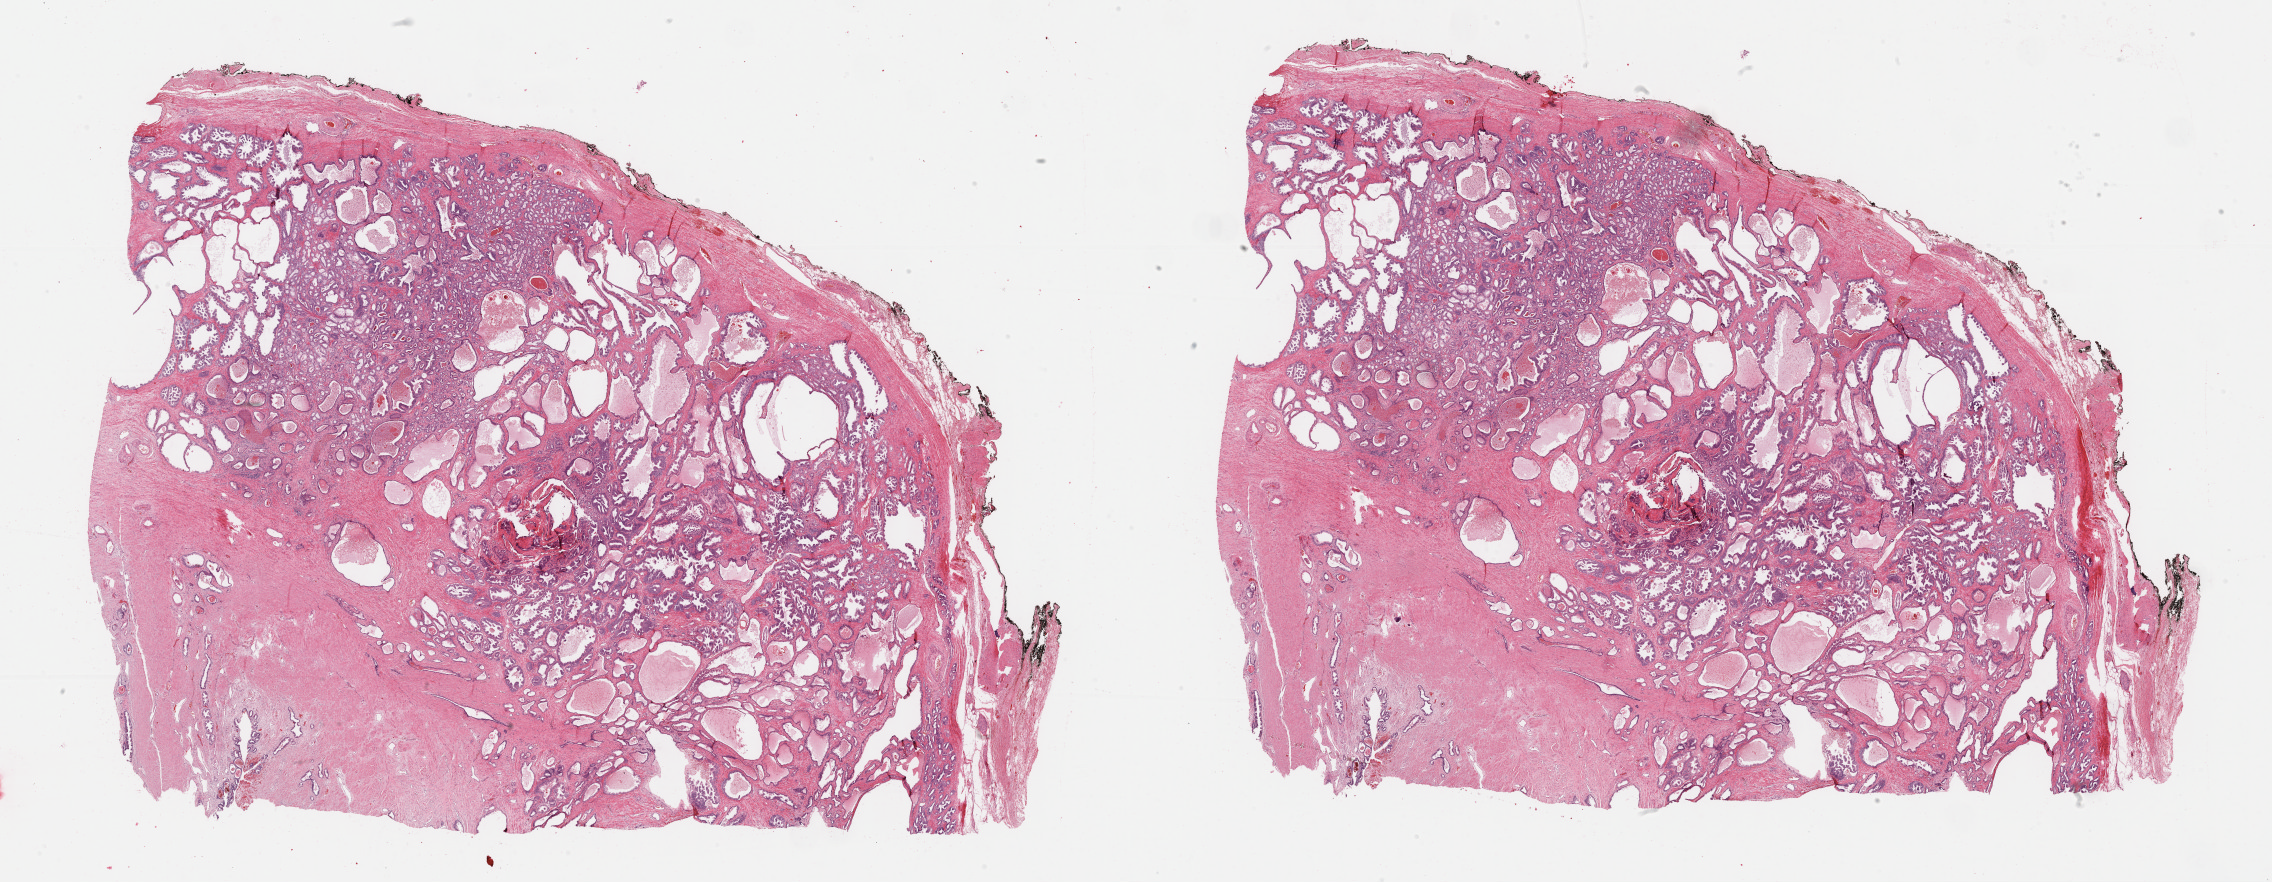
H&E-stained whole-slide image, whole scanned area (about 36.7 x 14.3 mm) shown as a low-resolution overview; FFPE section; sample: primary tumour, prostate. Male patient; age at initial diagnosis 71 years. Gleason score: 6 (3+3).
Pathologic diagnosis: Adenocarcinoma, NOS (prostate gland).